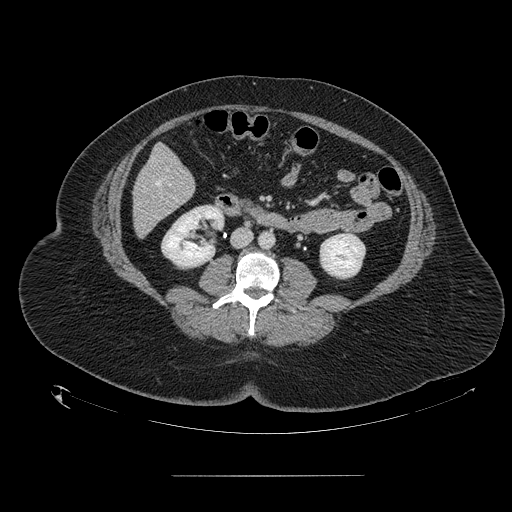
Contrast-enhanced abdominal CT, one axial slice; slice 40 of 164 in the series (ordered by position); soft-tissue window (W 400 / L 40 HU); 2.5 mm slice thickness; 512 × 512 image matrix, field of view 495 × 495 mm. Female patient, age 52 years. From the clinical record (not read from this slice): diagnosis: colorectal cancer liver metastases, imaged before liver resection; multiple liver metastases: yes; largest metastasis: 3.5 cm; chemotherapy before resection: no.
Structures marked on this image (manually delineated by an expert):
- hepatic veins: bounding box <156,181,161,186> (left, top, right, bottom; pixels)
- liver: <133,146,195,236>